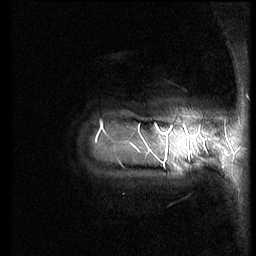
Breast MRI (dynamic contrast-enhanced), one sagittal slice; slice 11 of 66 in the series (ordered by position); dynamic contrast-enhanced series, image 2 of 3 at this slice position (ordered by acquisition); 1.5 T; TE 4.2 ms, TR 8.9 ms; 2.5 mm slice thickness; 256 × 256 image matrix, field of view 200 × 200 mm. Patient: female, 39 years. From the clinical record (not read from this slice): setting: breast cancer imaged before/during neoadjuvant chemotherapy; receptor status: HER2-positive.
Outlined on this slice (semi-automatic segmentation, software-assisted and operator-edited):
- analysis volume of interest (the breast-tissue region the enhancement analysis was run in; not a lesion): bounding box [x1, y1, x2, y2] px = [71, 76, 188, 212]
- tumour enhancement mask (voxels above the 140 % enhancement threshold inside the analysis volume of interest): [170, 127, 172, 130]